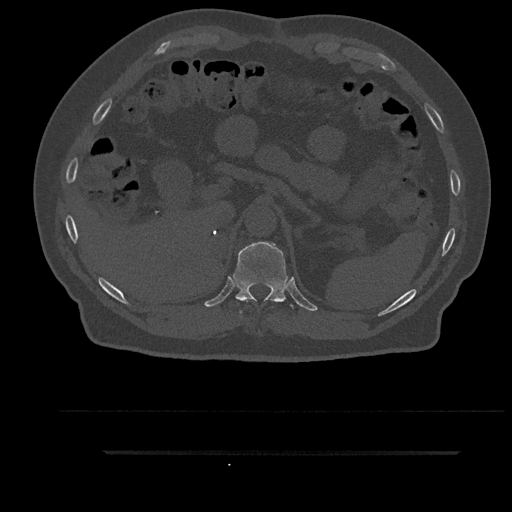
CT including the spine, one axial slice. Slice 323 of 797 in the series (ordered by position). 120 kVp. Bone window (W 1800 / L 400 HU). 512 × 512 image matrix, field of view 432 × 432 mm. Male patient, age 63 years. From the clinical record (not read from this slice): primary cancer: renal.
Outlined on this slice (semi-automatic segmentation, software-assisted and operator-edited):
- T11 vertebra: bounding box <233,242,293,313> (left, top, right, bottom; pixels)